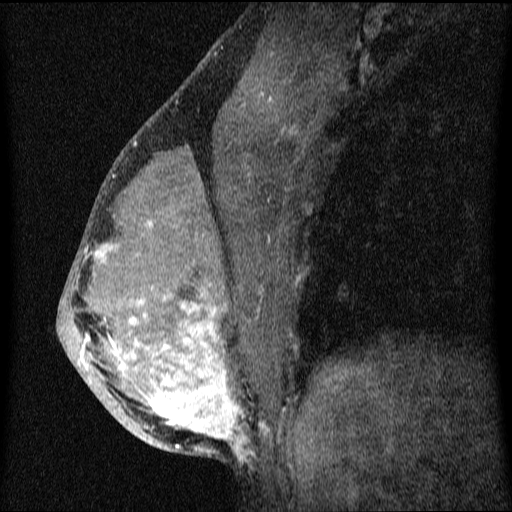
Breast MRI (dynamic contrast-enhanced), one sagittal slice. Dynamic contrast-enhanced series, image 2 of 4 at this slice position (ordered by acquisition). 1.5 T. TE 4.2 ms, TR 9.1 ms. 512 × 512 image matrix, field of view 180 × 180 mm. Female patient, age 33 years.
Structures marked on this image (semi-automatic segmentation, software-assisted and operator-edited):
- analysis volume of interest (the breast-tissue region the enhancement analysis was run in; not a lesion): bounding box <58,151,336,458> (left, top, right, bottom; pixels)
- tumour enhancement mask (voxels above the 70 % enhancement threshold inside the analysis volume of interest): <81,222,251,458>